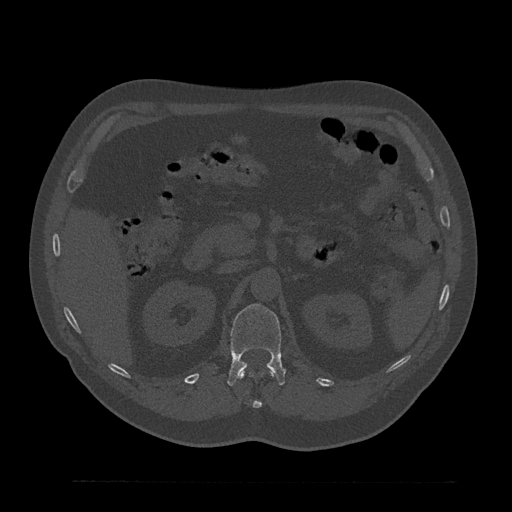
CT including the spine, one axial slice. Position 186 of 797 along the scan axis. Bone window (W 1800 / L 400 HU). 512 × 512 image matrix. Male patient, age 61 years. From the clinical record (not read from this slice): primary cancer: prostate.
Outlined on this slice (semi-automatically segmented with operator editing):
- L1 vertebra: bounding box [x1, y1, x2, y2] px = [227, 304, 285, 386]
- T12 vertebra: [239, 371, 274, 409]